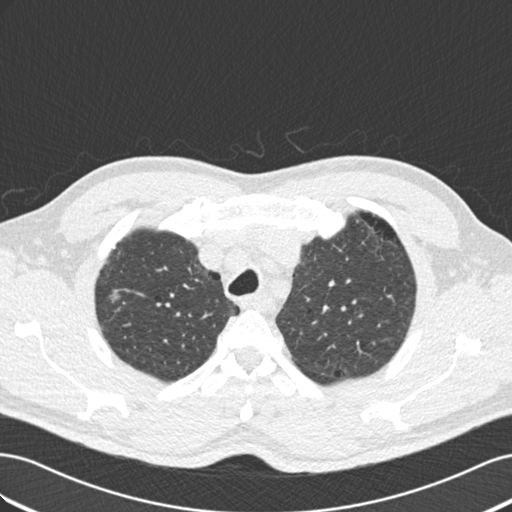
Axial slice from a low-dose chest CT screening exam; second screening round (one year after baseline); lung window (W 1500 / L -600 HU); 2 mm slice thickness. Male, age 56 years at enrolment.
Expert-annotated lung lesion, bounding box (x1, y1, x2, y2) in pixels: (79, 282, 130, 321). Reader record for this screening exam (exam-level; its link to the box is not recorded): non-calcified nodule or mass ≥4 mm, right upper lobe, 13 × 12 mm, smooth margins, mixed attenuation, pre-existing on the prior screen: yes; interval growth: yes. Official screen result: positive, change unspecified: nodule(s) >= 4 mm or enlarging nodule(s), mass(es), or other non-specific abnormalities suspicious for lung cancer. Participant outcome: lung cancer diagnosed 174 days after this screen — bronchiolo-alveolar carcinoma, non-mucinous, right upper lobe, moderately differentiated (G2), stage IIIB (AJCC 6th edition), 10 mm at pathology.